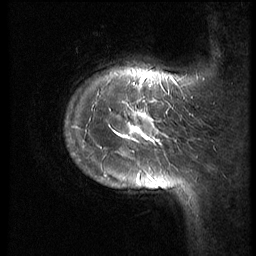
Breast MRI (dynamic contrast-enhanced), one sagittal slice; 3 images stored at this slice position (order not interpretable as contrast timing); 1.5 T; TE 4.2 ms, TR 9 ms; 2.5 mm slice thickness; 256 × 256 image matrix, field of view 180 × 180 mm. Patient: female, 28 years. Case-level facts recorded for this patient, not image findings: setting: breast cancer imaged before/during neoadjuvant chemotherapy.
Structures marked on this image (semi-automatic segmentation, software-assisted and operator-edited):
- analysis volume of interest (the breast-tissue region the enhancement analysis was run in; not a lesion): bounding box <63,43,186,214> (left, top, right, bottom; pixels)
- tumour enhancement mask (voxels above the 140 % enhancement threshold inside the analysis volume of interest): <77,78,173,190>